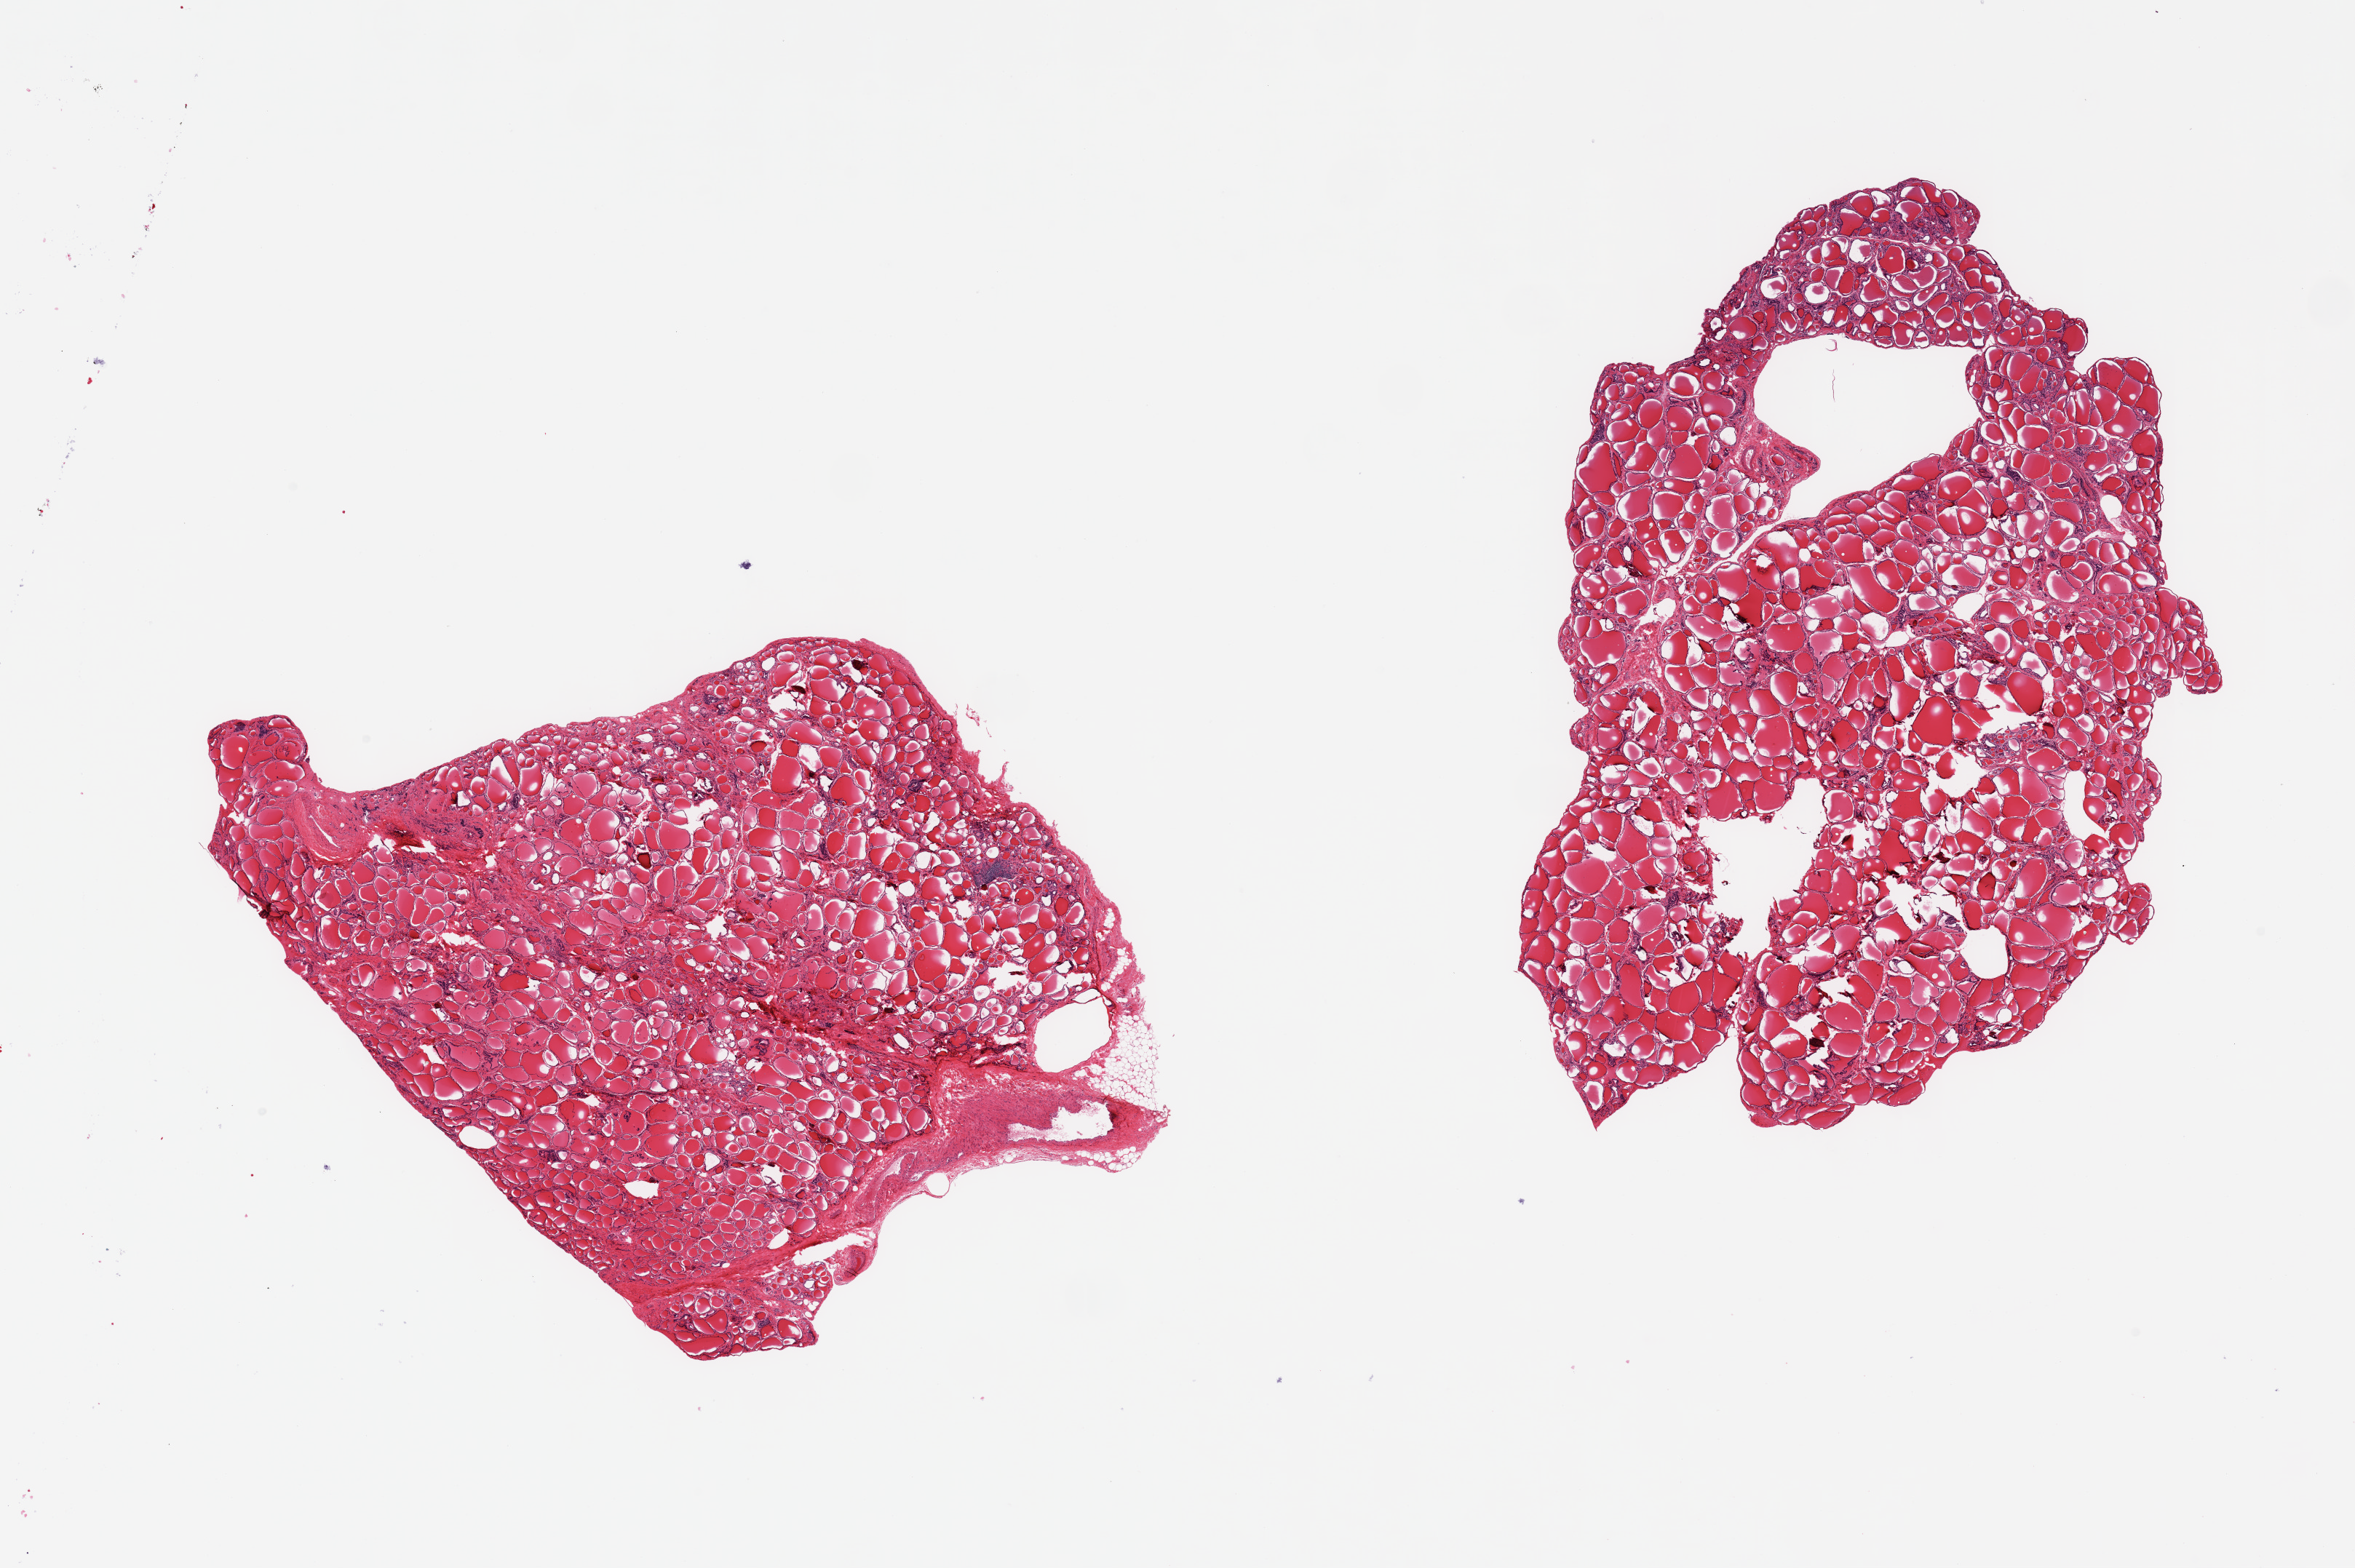
Haematoxylin and eosin whole-slide image, brightfield — shown as a low-resolution overview of the whole scanned area (about 25.6 x 17.0 mm). PAXgene-fixed paraffin-embedded (PFPE) section. Target tissue: thyroid. Tissue donor sample. Donor sex: male.
- pathologist's review note for this sample: 2 pieces, no abnormalities